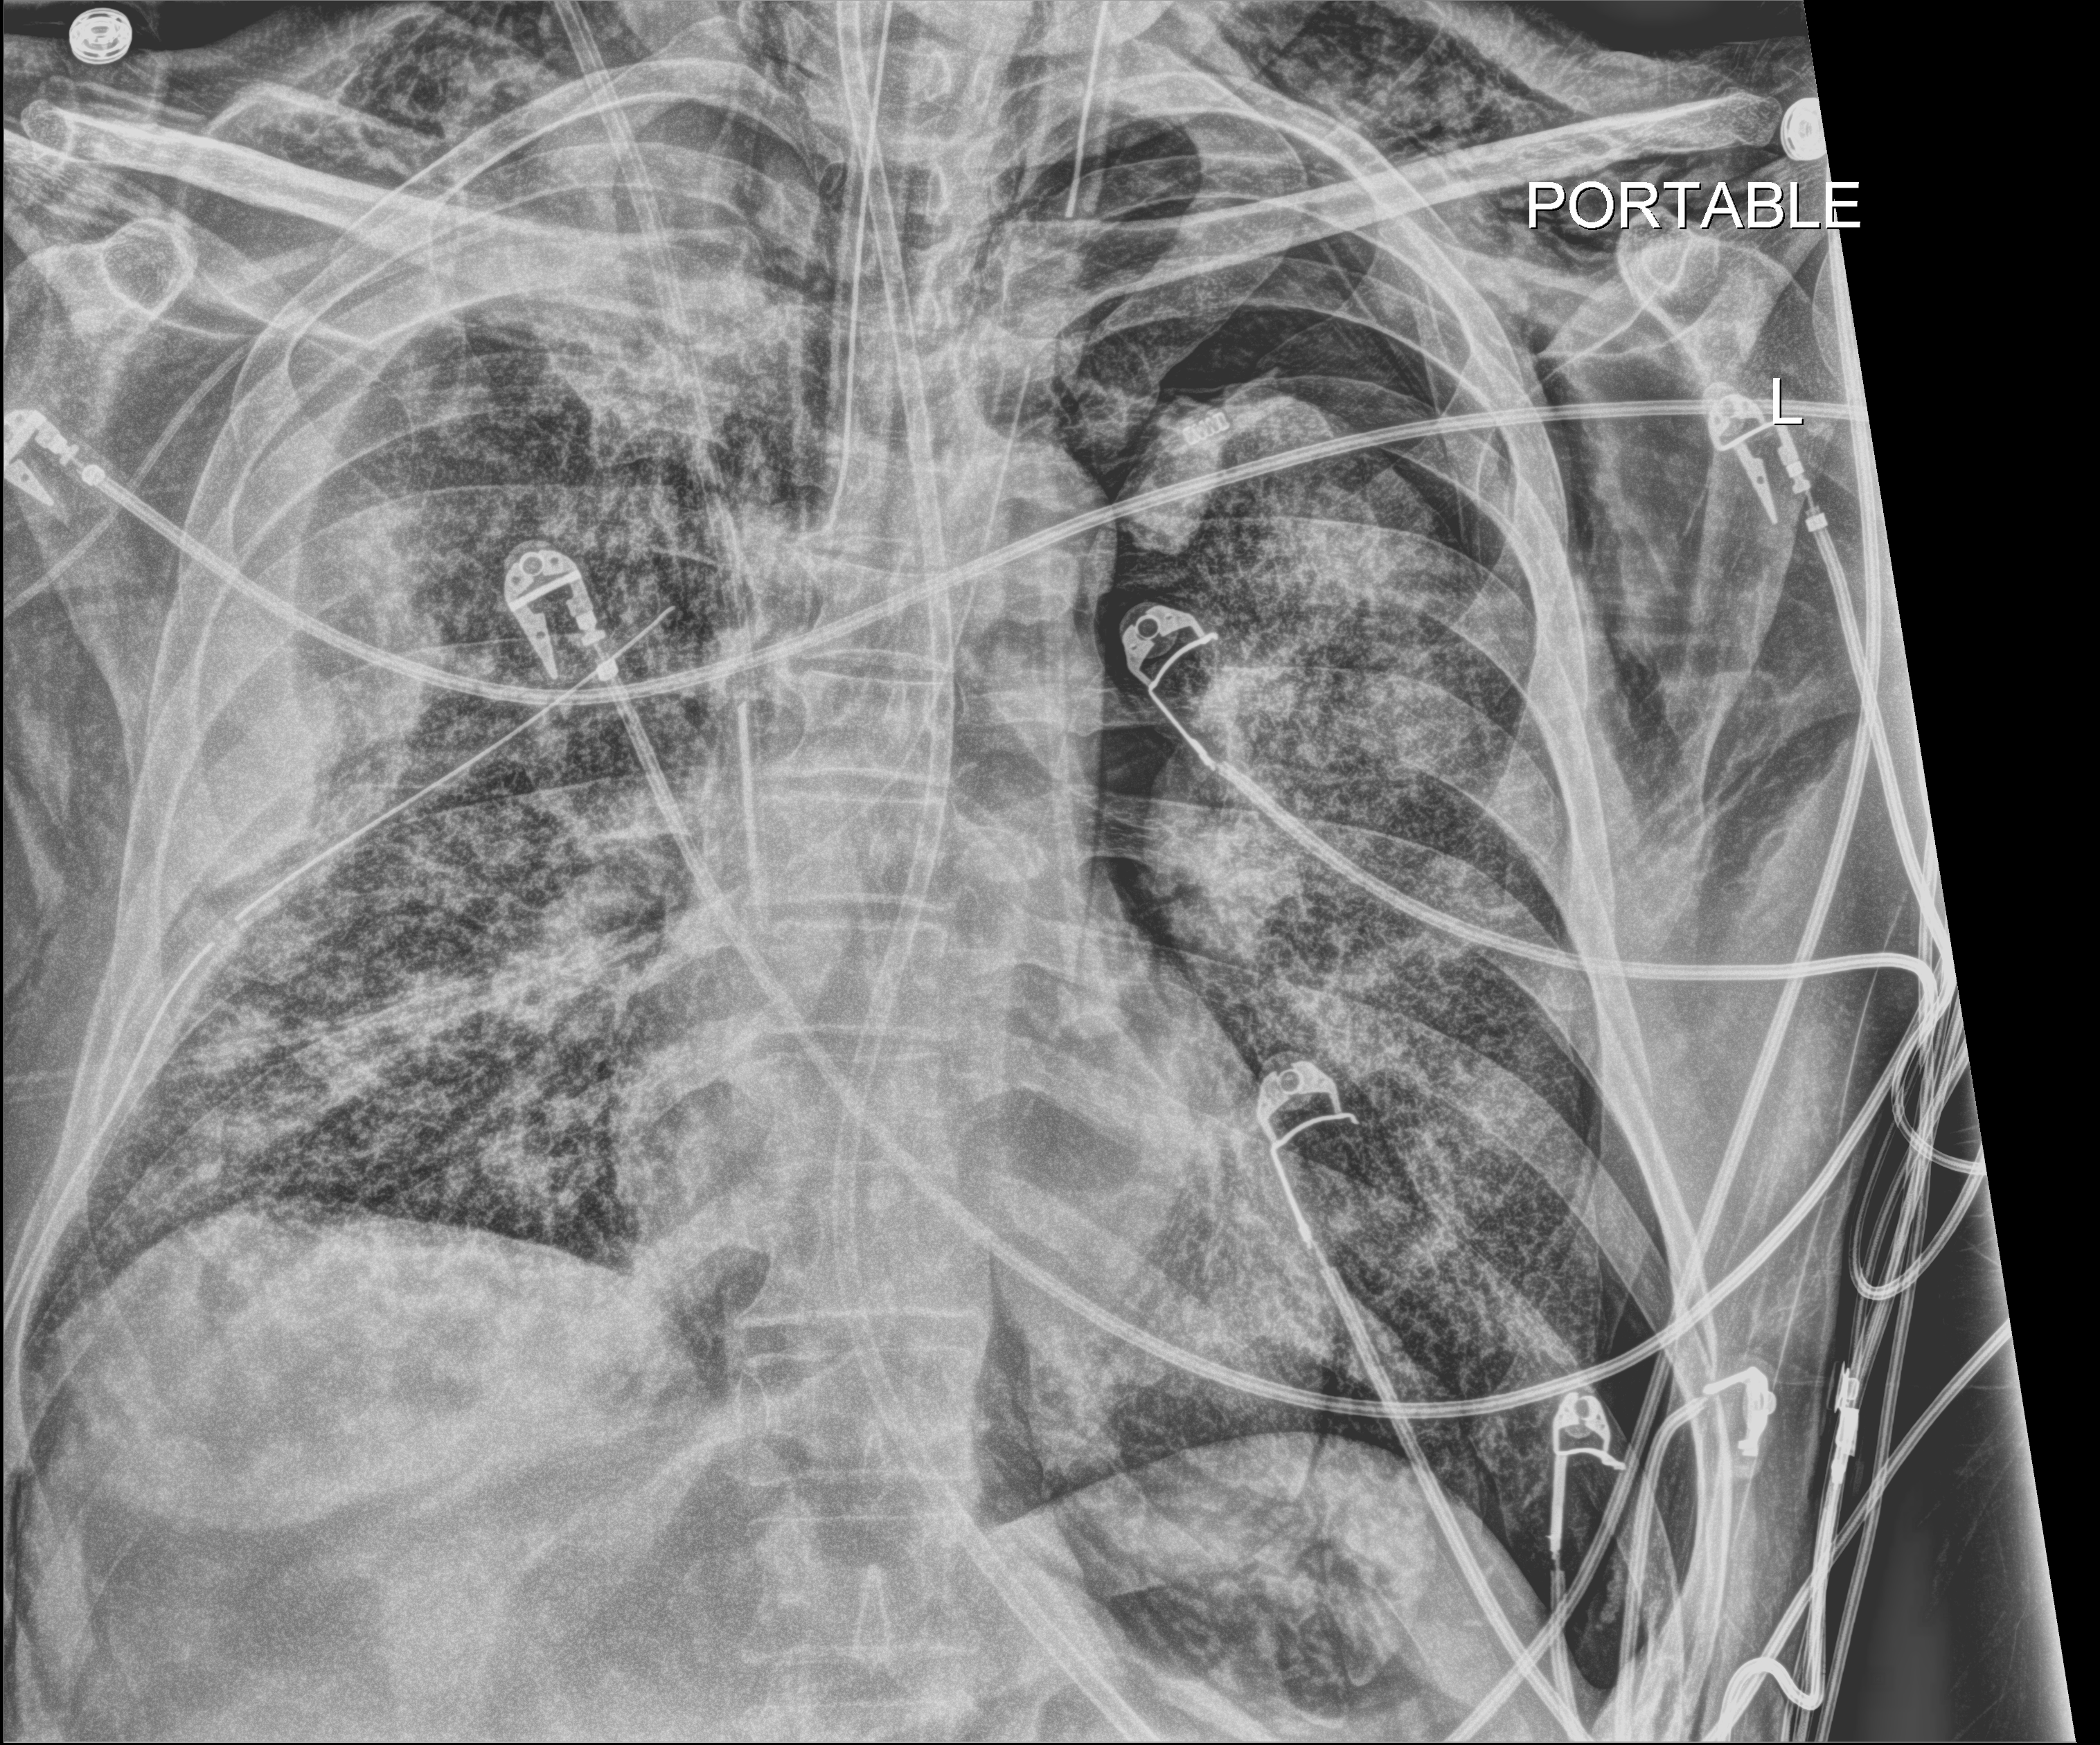
Chest X-ray (portable), anteroposterior (AP) projection. Patient hospitalised with COVID-19; male, aged 18–59 years.
Admission-level facts for this patient (not findings on this image; timing relative to this image not recorded): other chronic lung disease (admission record): no; mechanically ventilated during this hospital stay: yes; diabetes (admission record): no.